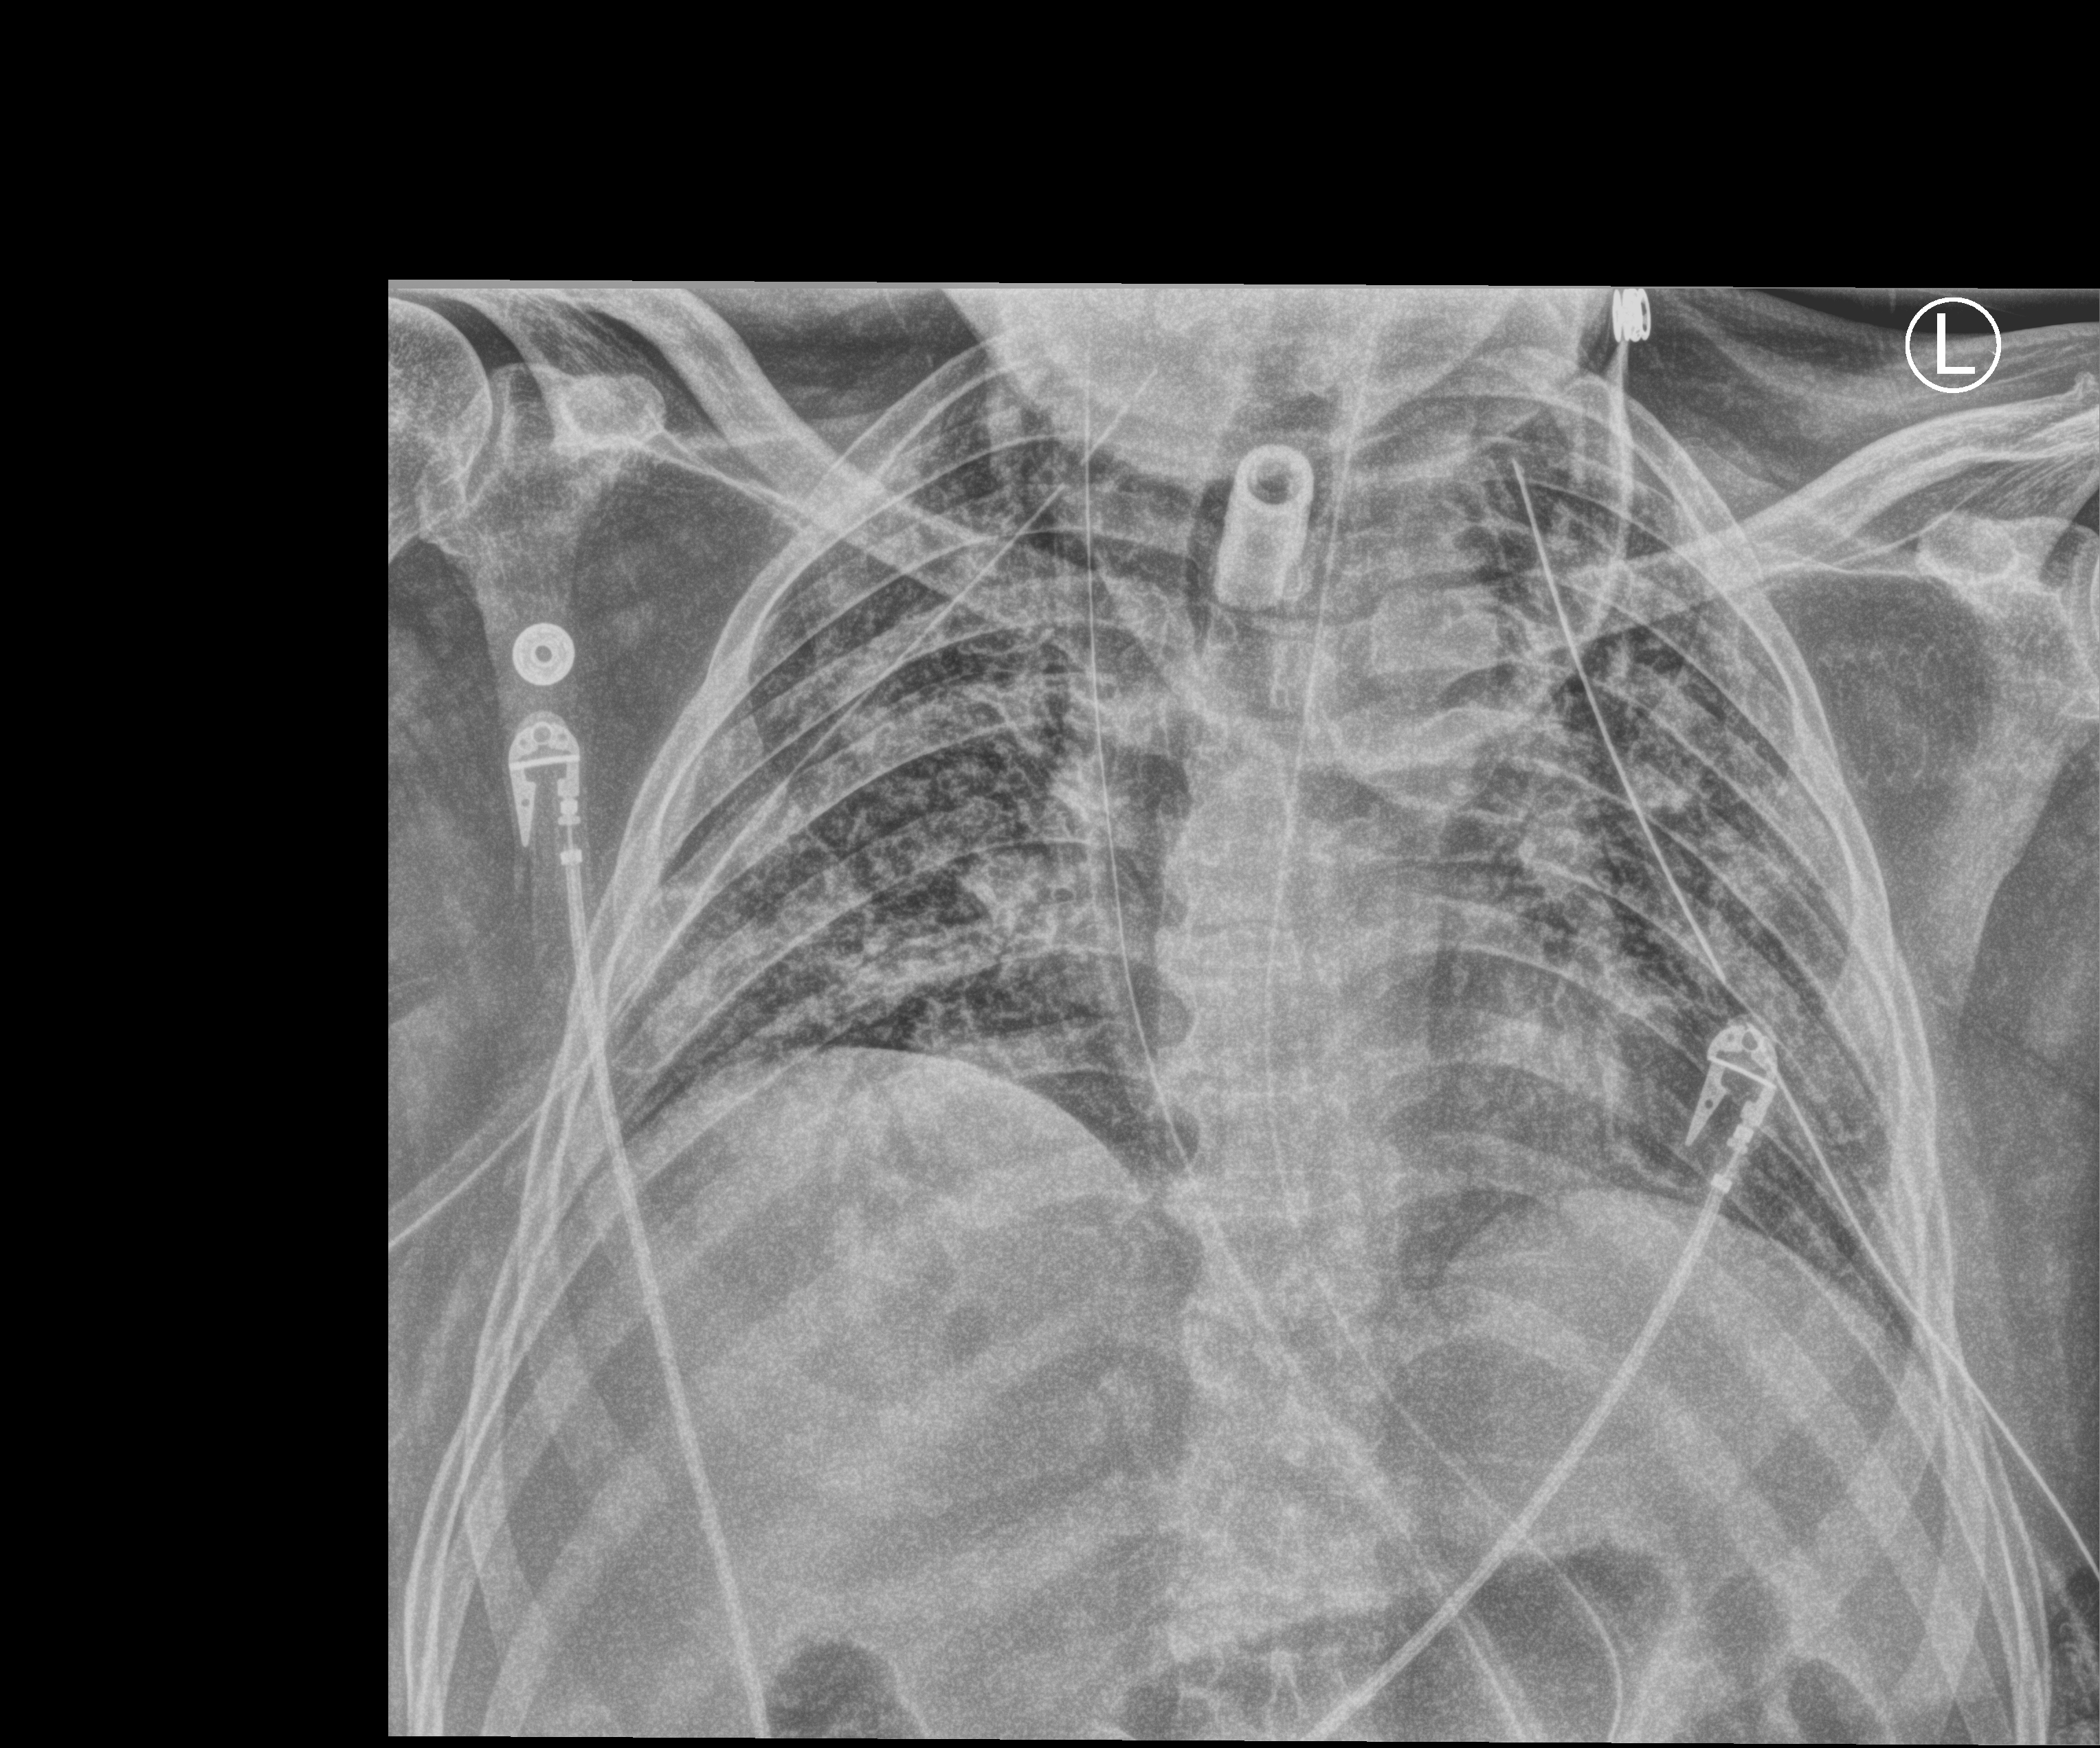
Bedside chest radiograph (computed radiography); anteroposterior (AP) projection. Patient hospitalised with COVID-19; male, aged 18–59 years.
From the hospital-stay record, not from the radiograph (when in the stay this image was taken is not recorded):
- admitted to intensive care during this hospital stay: yes
- mechanically ventilated during this hospital stay: yes